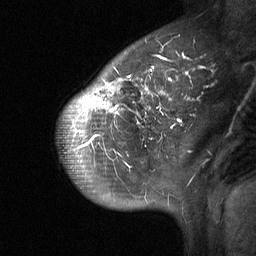
Breast MRI (dynamic contrast-enhanced), one sagittal slice; dynamic contrast-enhanced study with each time point stored as its own series, time point 2 of 3 at this slice position (early post-contrast, ordered by acquisition time); 1.5 T; TE 4.8 ms, TR 27 ms; 2 mm slice thickness; 256 × 256 image matrix, field of view 200 × 200 mm. Patient: female, 42 years. From the clinical record (not read from this slice): setting: breast cancer imaged before/during neoadjuvant chemotherapy; receptor status: triple-negative.
Annotated regions visible in this slice (semi-automatic segmentation, software-assisted and operator-edited):
- analysis volume of interest (the breast-tissue region the enhancement analysis was run in; not a lesion): bounding box (x1, y1, x2, y2) in pixels: (57, 30, 203, 190)
- tumour enhancement mask (voxels above the 90 % enhancement threshold inside the analysis volume of interest): (73, 55, 185, 156)